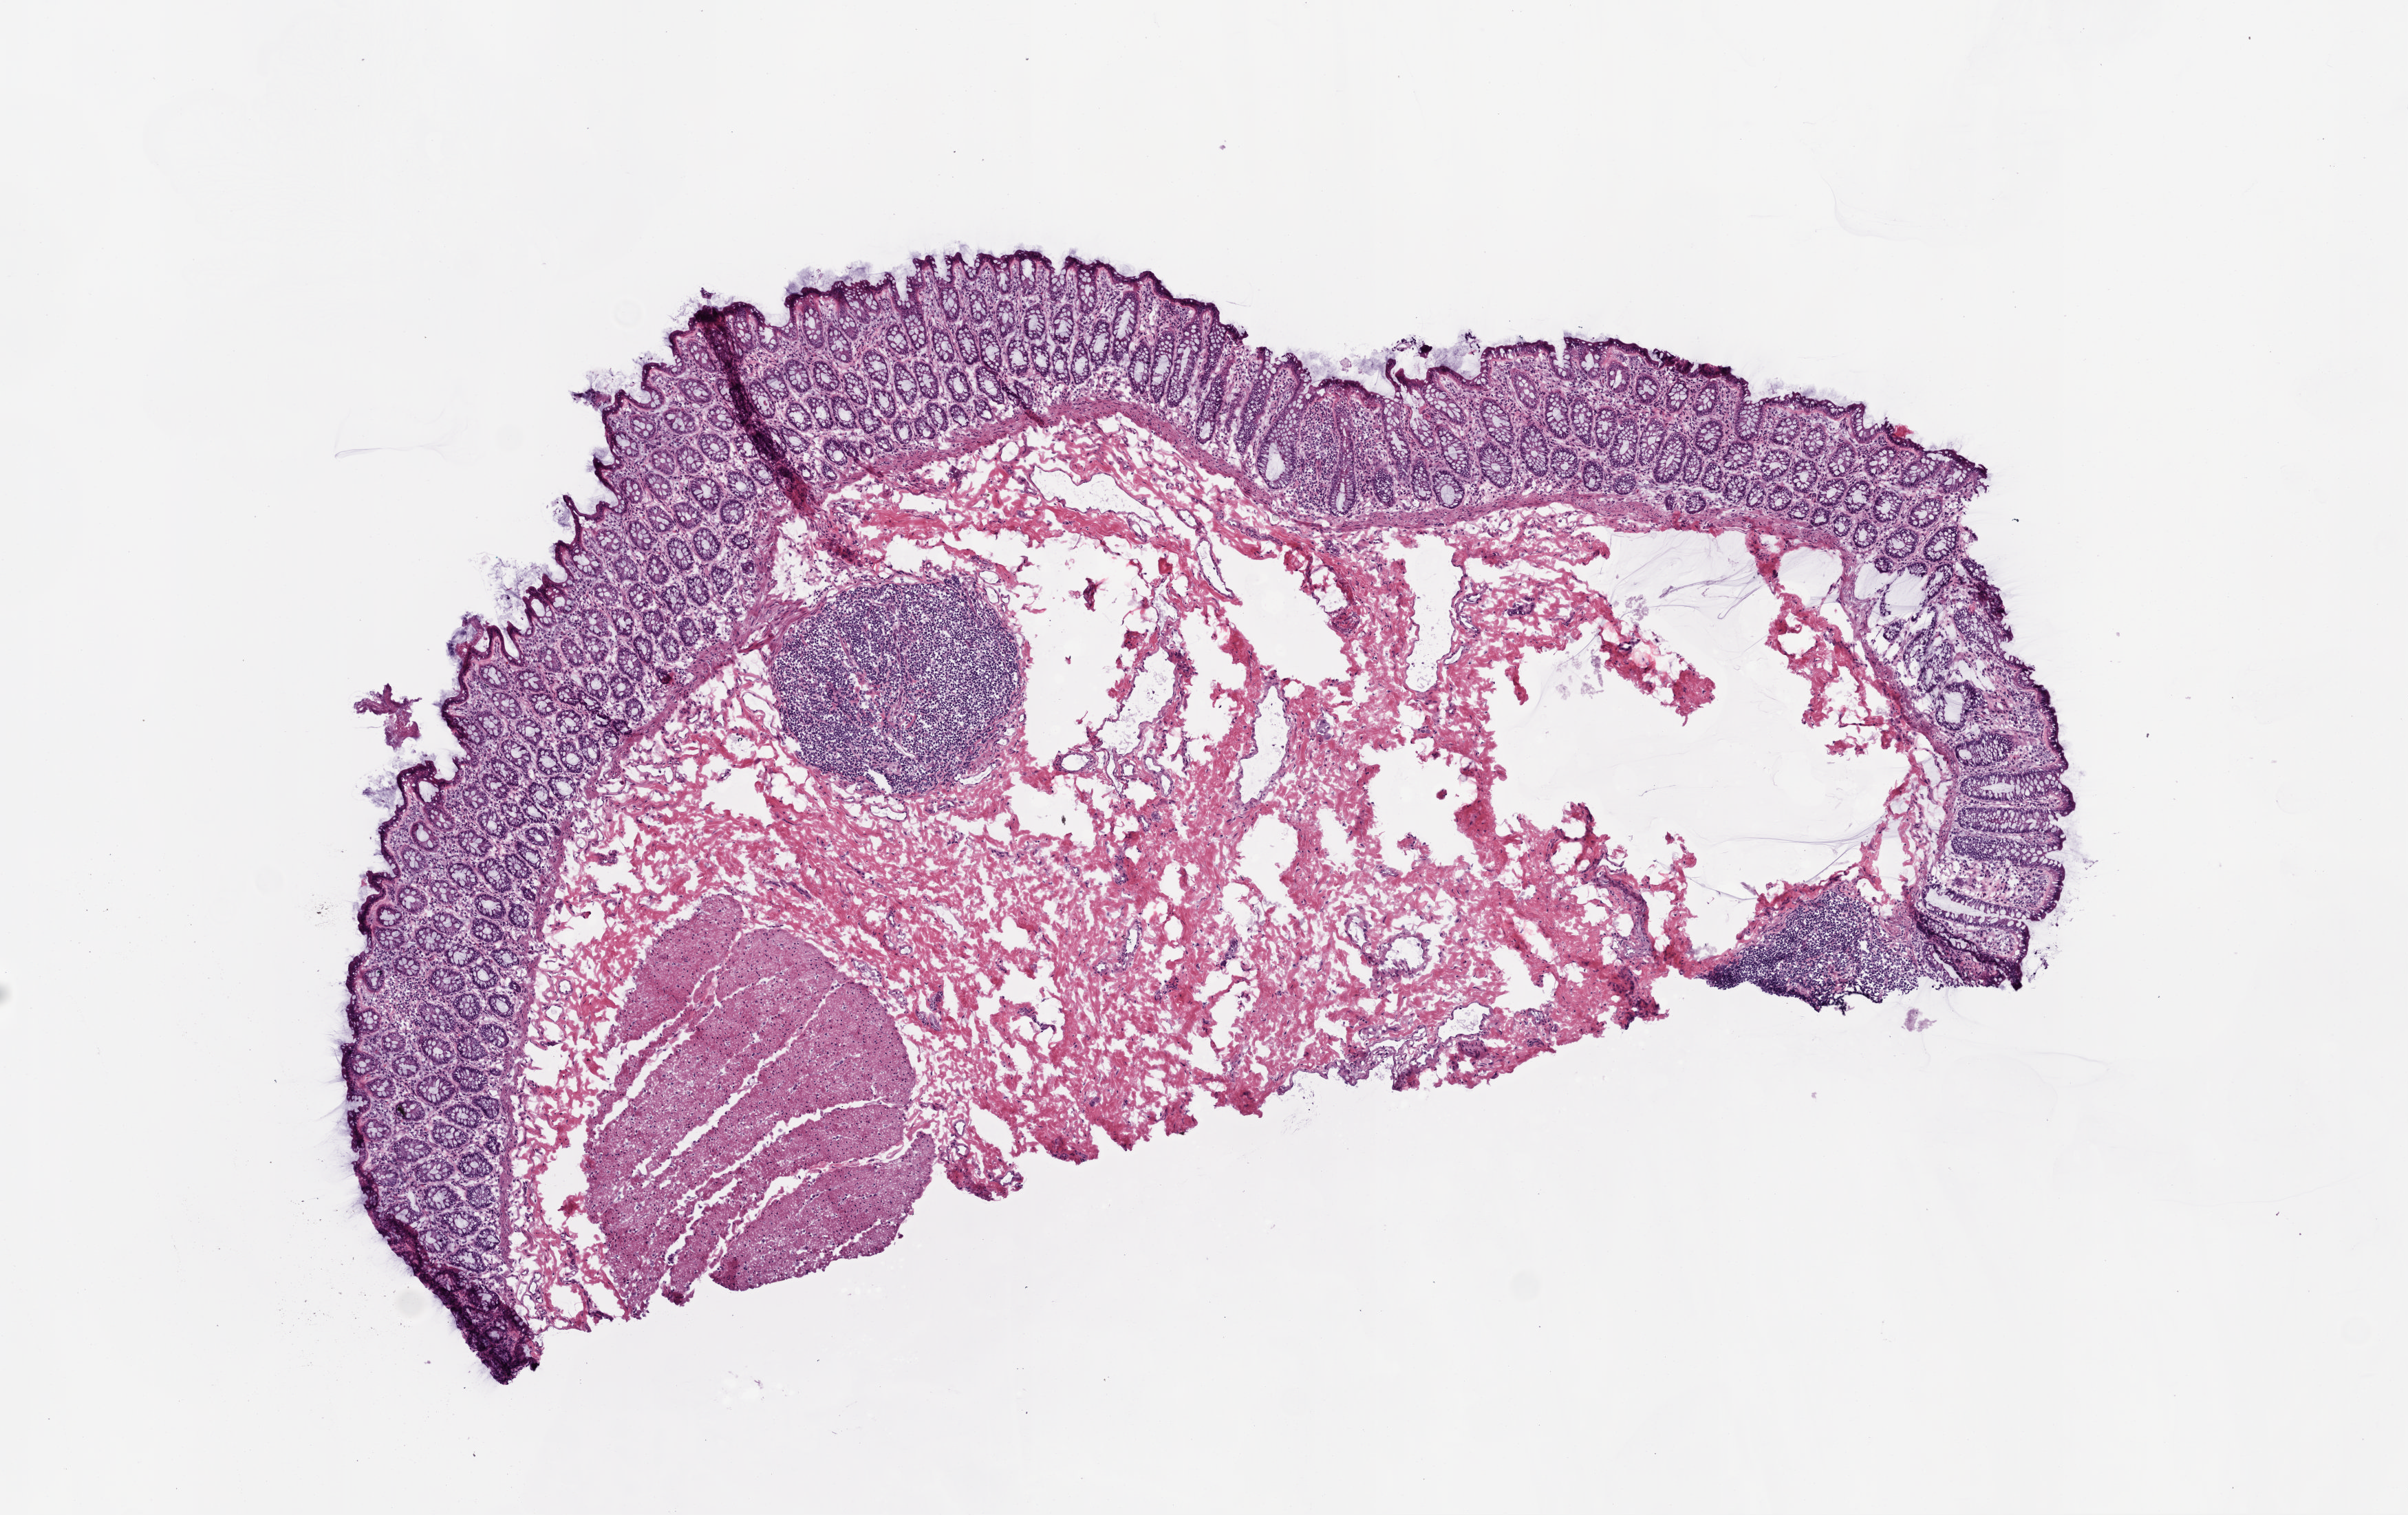
Digitized Hematoxylin and eosin (H&E) stained tissue section (whole slide) — shown as a low-resolution overview of the whole scanned area (about 7.0 x 4.4 mm, slide scanned at 20x); frozen section from the top of the tissue portion; solid tissue normal (non-tumour tissue) sample from the colon. Patient: male, age at initial diagnosis 57 years.
This section: solid tissue normal (non-tumour) sample from the same patient. Patient diagnosis: Adenocarcinoma, NOS.